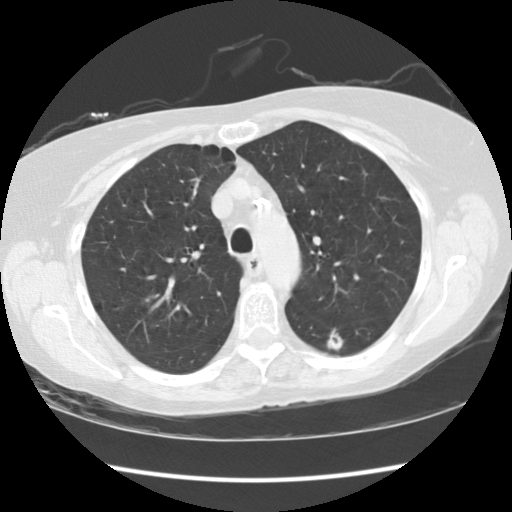
Low-dose screening chest CT, one axial slice; slice 87 of 119 in the series (ordered by position); reconstruction kernel STANDARD; lung window (W 1500 / L -600 HU); 2.5 mm slice thickness; 512 × 512 image matrix, field of view 334 × 334 mm.
Structures marked on this image (expert manual segmentation):
- lesion 1 (tumor, lower lobe of left lung): box from (x=327, y=329) to (x=343, y=351) px